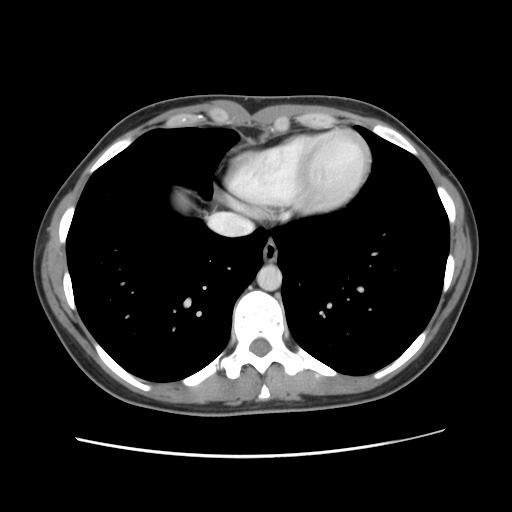
Contrast-enhanced abdominal CT, one axial slice. Slice 121 of 134 in the series (ordered by position). Soft-tissue window (W 400 / L 40 HU). 512 × 512 image matrix, field of view 339 × 339 mm. Female patient, age 33 years. From the clinical record (not read from this slice): diagnosis: colorectal cancer liver metastases, imaged before liver resection; multiple liver metastases: yes; largest metastasis: 4.5 cm; disease in both lobes: yes.
Outlined on this slice (outlined manually by an expert reader):
- liver: bounding box <170,192,191,210> (left, top, right, bottom; pixels)
- planned liver remnant (the part of the liver to remain after resection): <171,192,190,210>